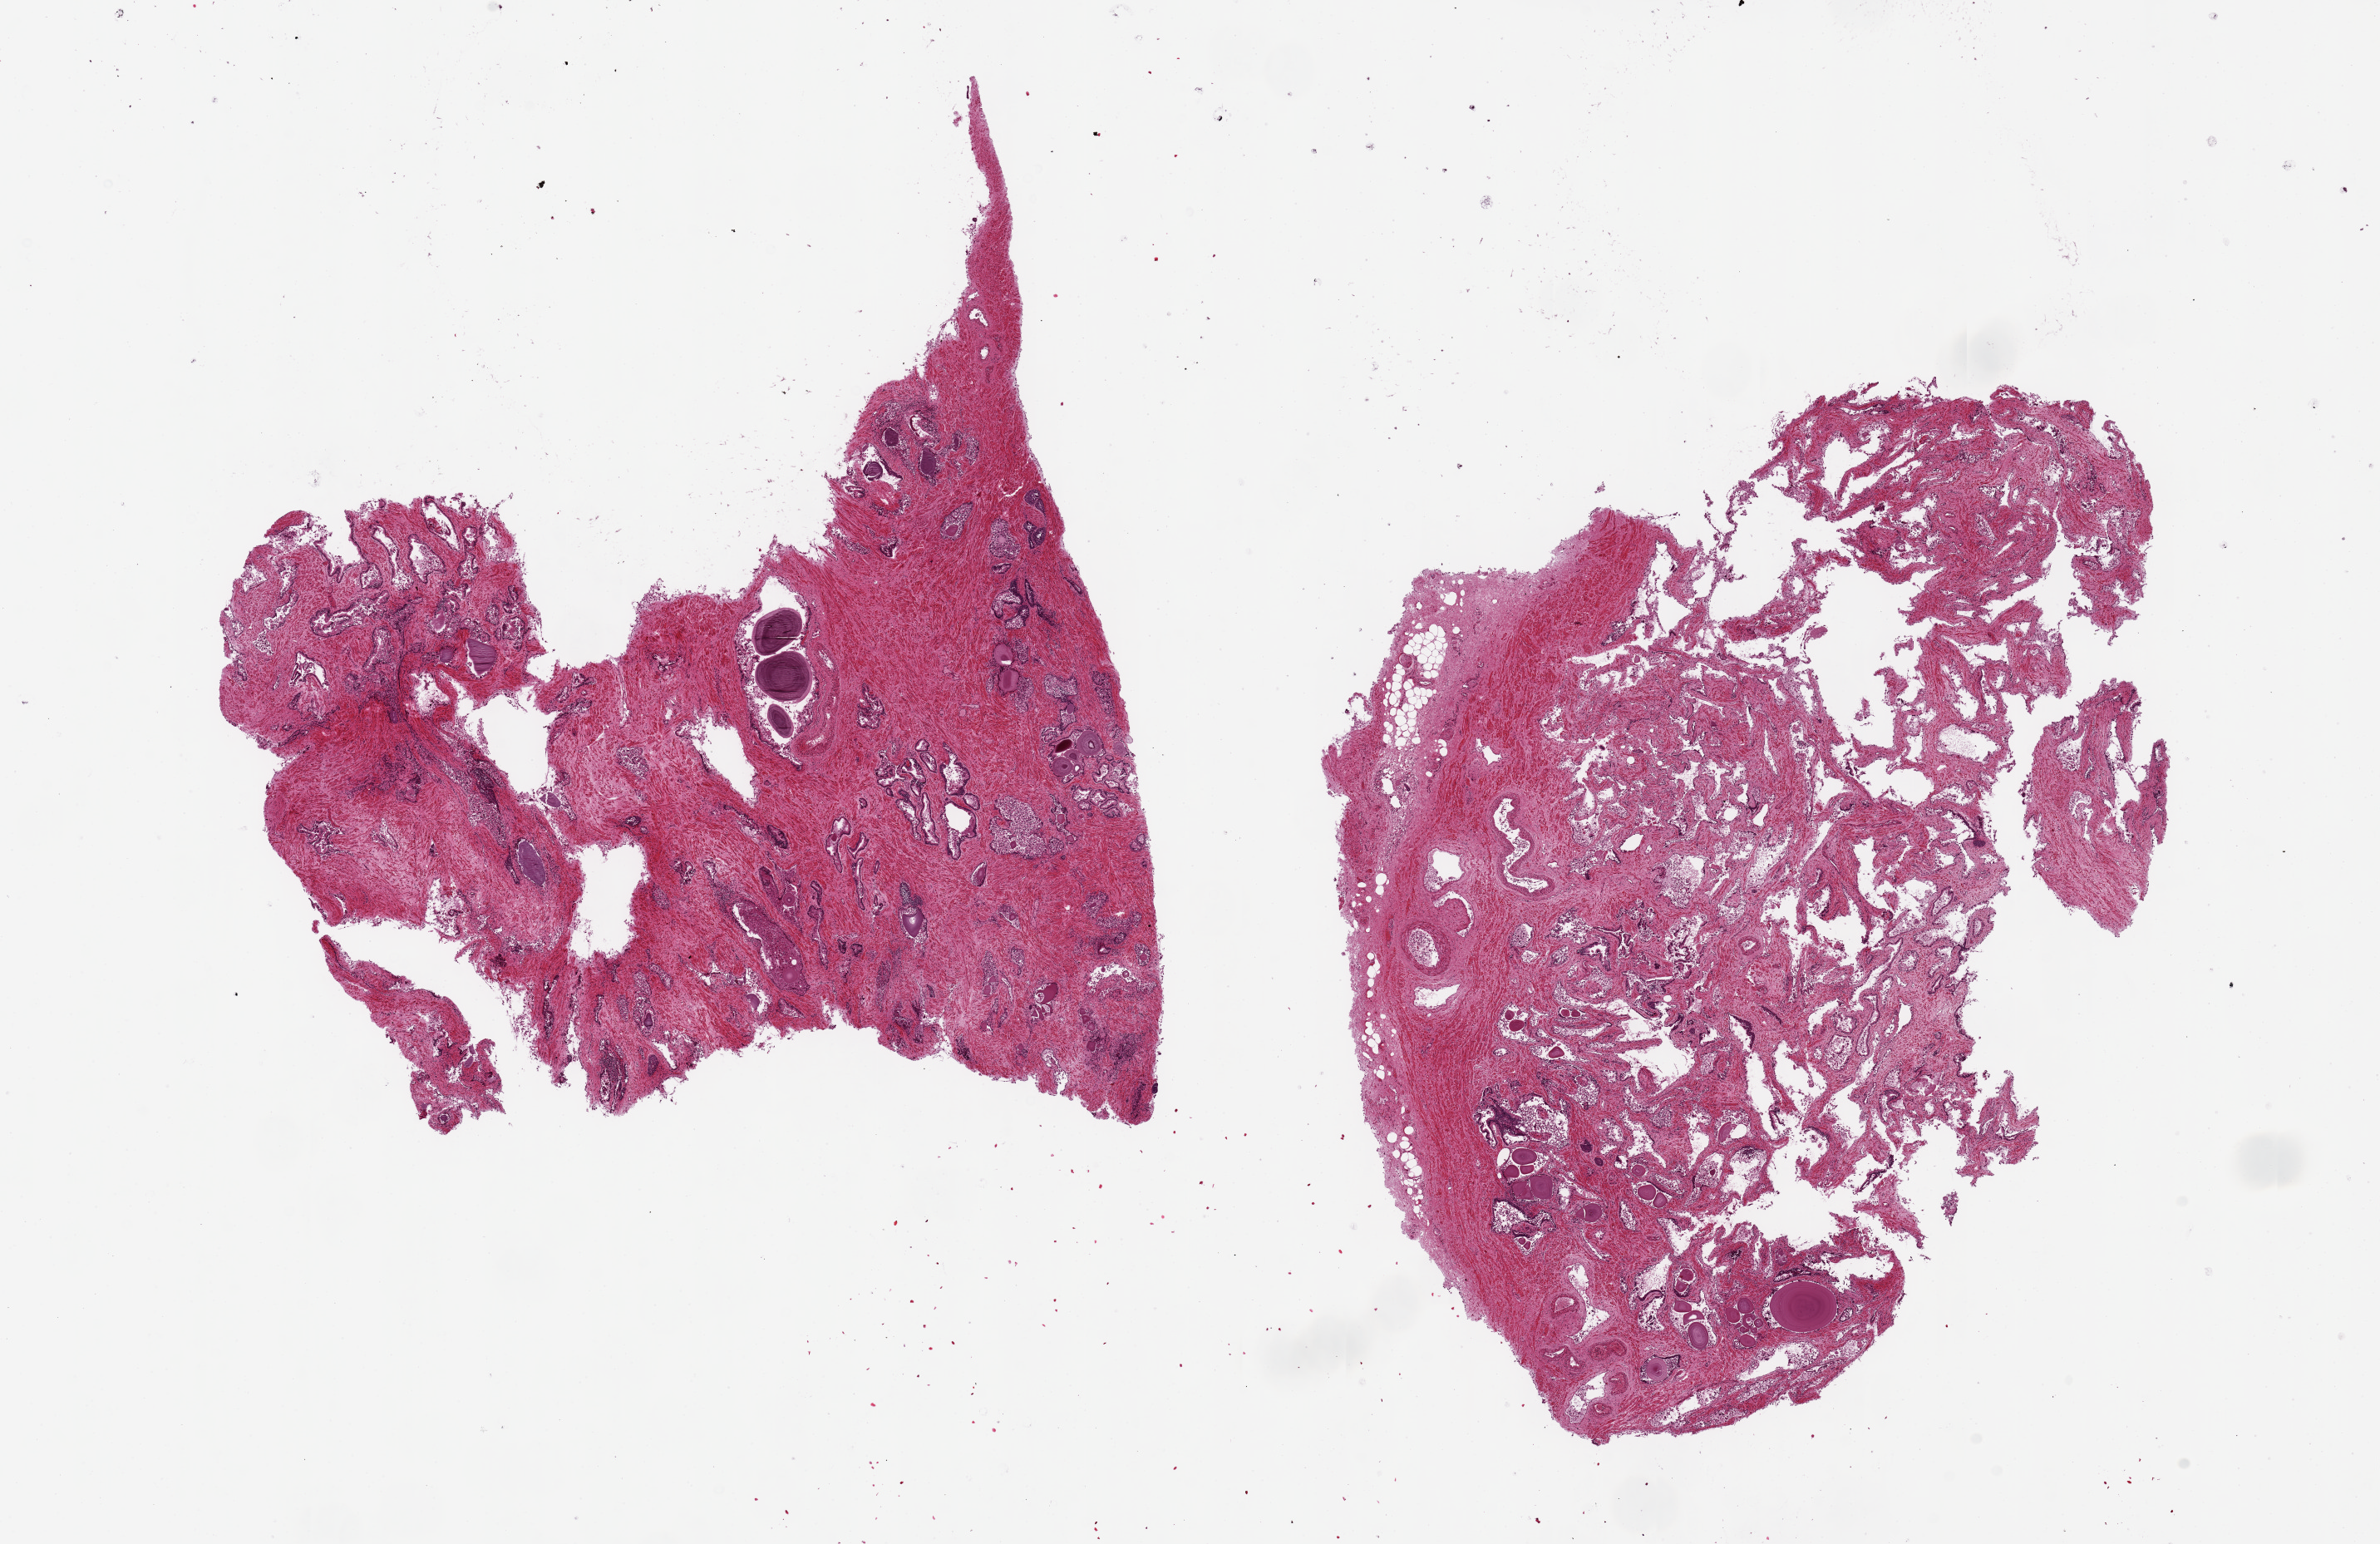
Digitized haematoxylin and eosin-stained section, brightfield, a low-resolution overview of the entire scanned area, about 22.6 x 14.7 mm (slide scanned at 20x). PAXgene-fixed paraffin-embedded (PFPE) section. Section of prostate (target tissue). Tissue donor sample. Donor: male.
Pathologist's review note for this sample: 2 pieces 10x8 & 8x5.9mm; glandular mucosa badly autolyzed.